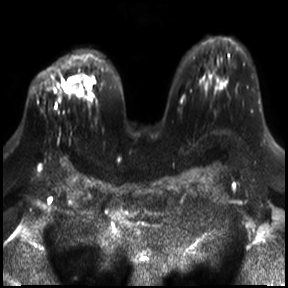
Breast MRI, one axial slice; slice 20 of 30 in the series (ordered by position); diffusion-weighted series; image 2 of 4 stored at this slice position (different b-values; order by instance number); 3 T; 4 mm slice thickness; 288 × 288 image matrix, field of view 340 × 340 mm. Female patient.
Annotated regions visible in this slice (outlined manually by an expert reader):
- tumour on diffusion-weighted imaging: bounding box <56,77,84,103> (left, top, right, bottom; pixels)